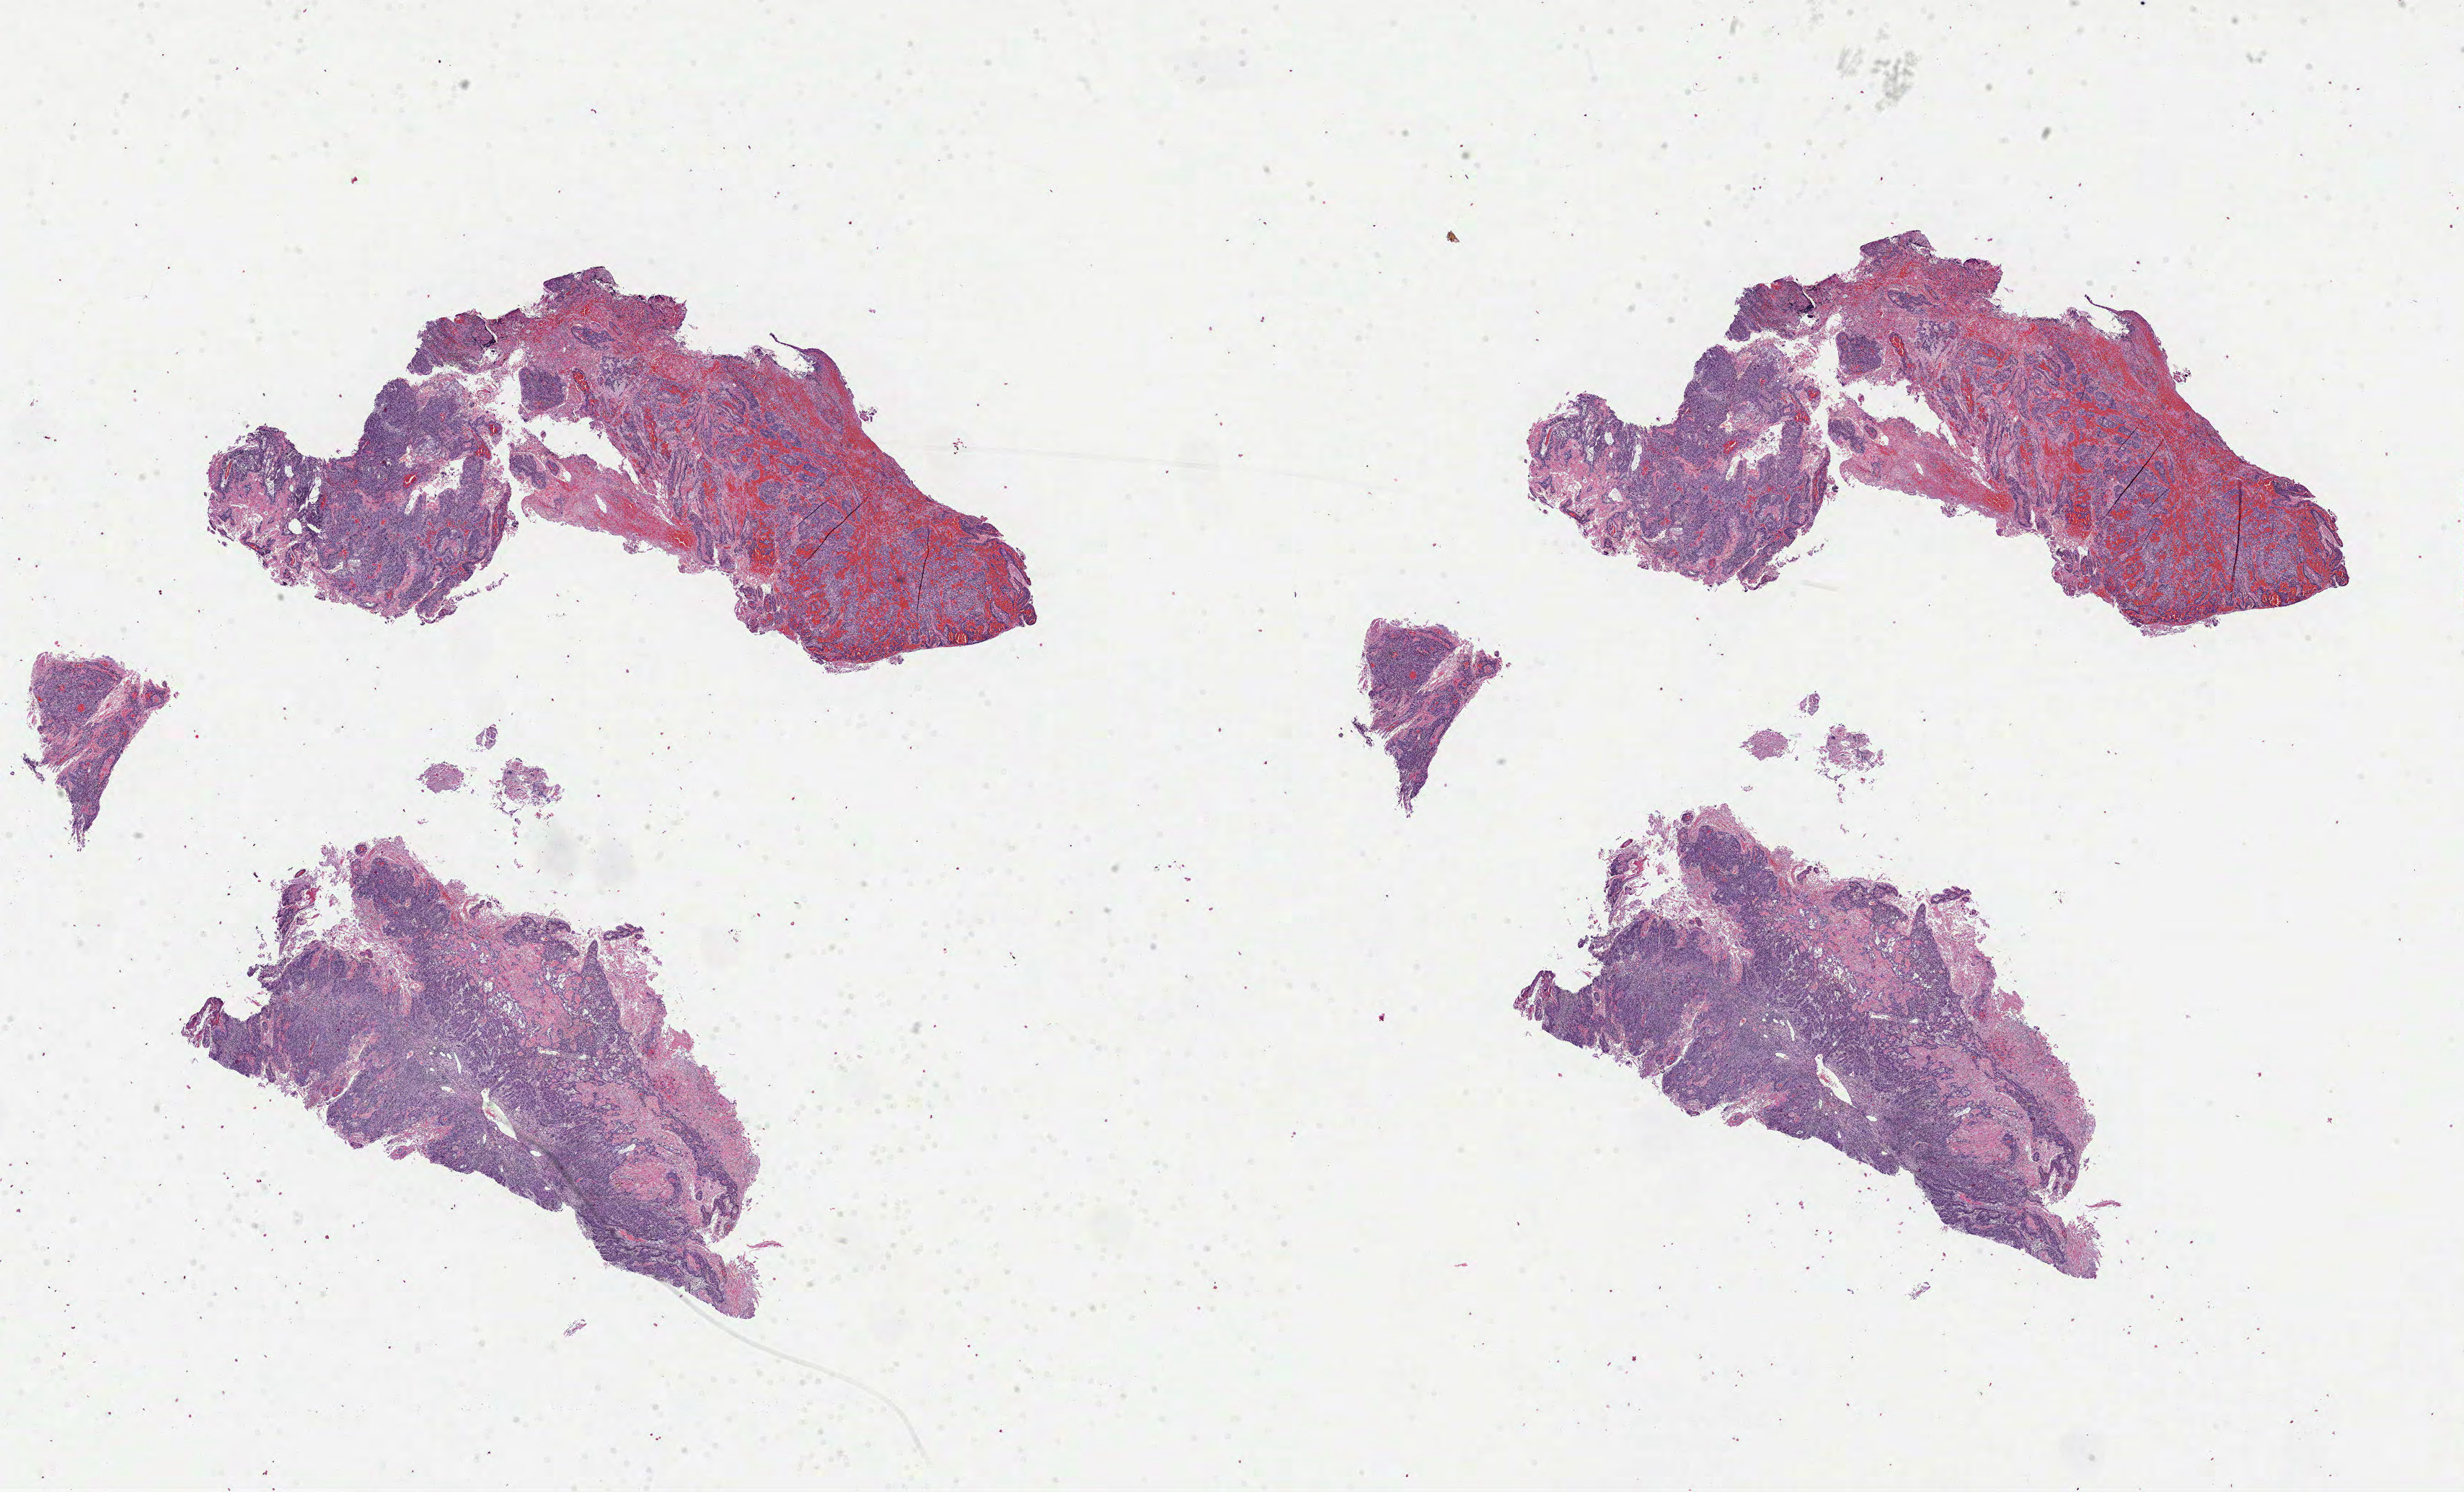
Digitized Hematoxylin and eosin (H&E) stained tissue section (whole slide), whole scanned area (about 27.6 x 16.7 mm, from a 40x scan) shown as a low-resolution overview, FFPE section, head and neck, primary tumour sample. Patient: male, age at initial diagnosis 62 years. Histologic grade: G2 (moderately differentiated).
AJCC pathologic stage: IVA (7th edition). Diagnosis: Squamous cell carcinoma, NOS (overlapping lesion of lip, oral cavity and pharynx).